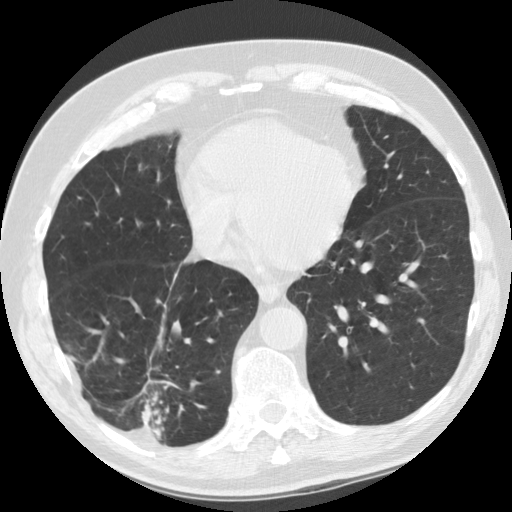
Low-dose screening chest CT, one axial slice. Slice 39 of 135 in the series (ordered by position). Reconstruction kernel STANDARD. Lung window (W 1500 / L -600 HU). 512 × 512 image matrix.
Outlined on this slice (expert manual segmentation):
- lesion 1 (tumor, lower lobe of right lung): bounding box <142,395,169,439> (left, top, right, bottom; pixels)